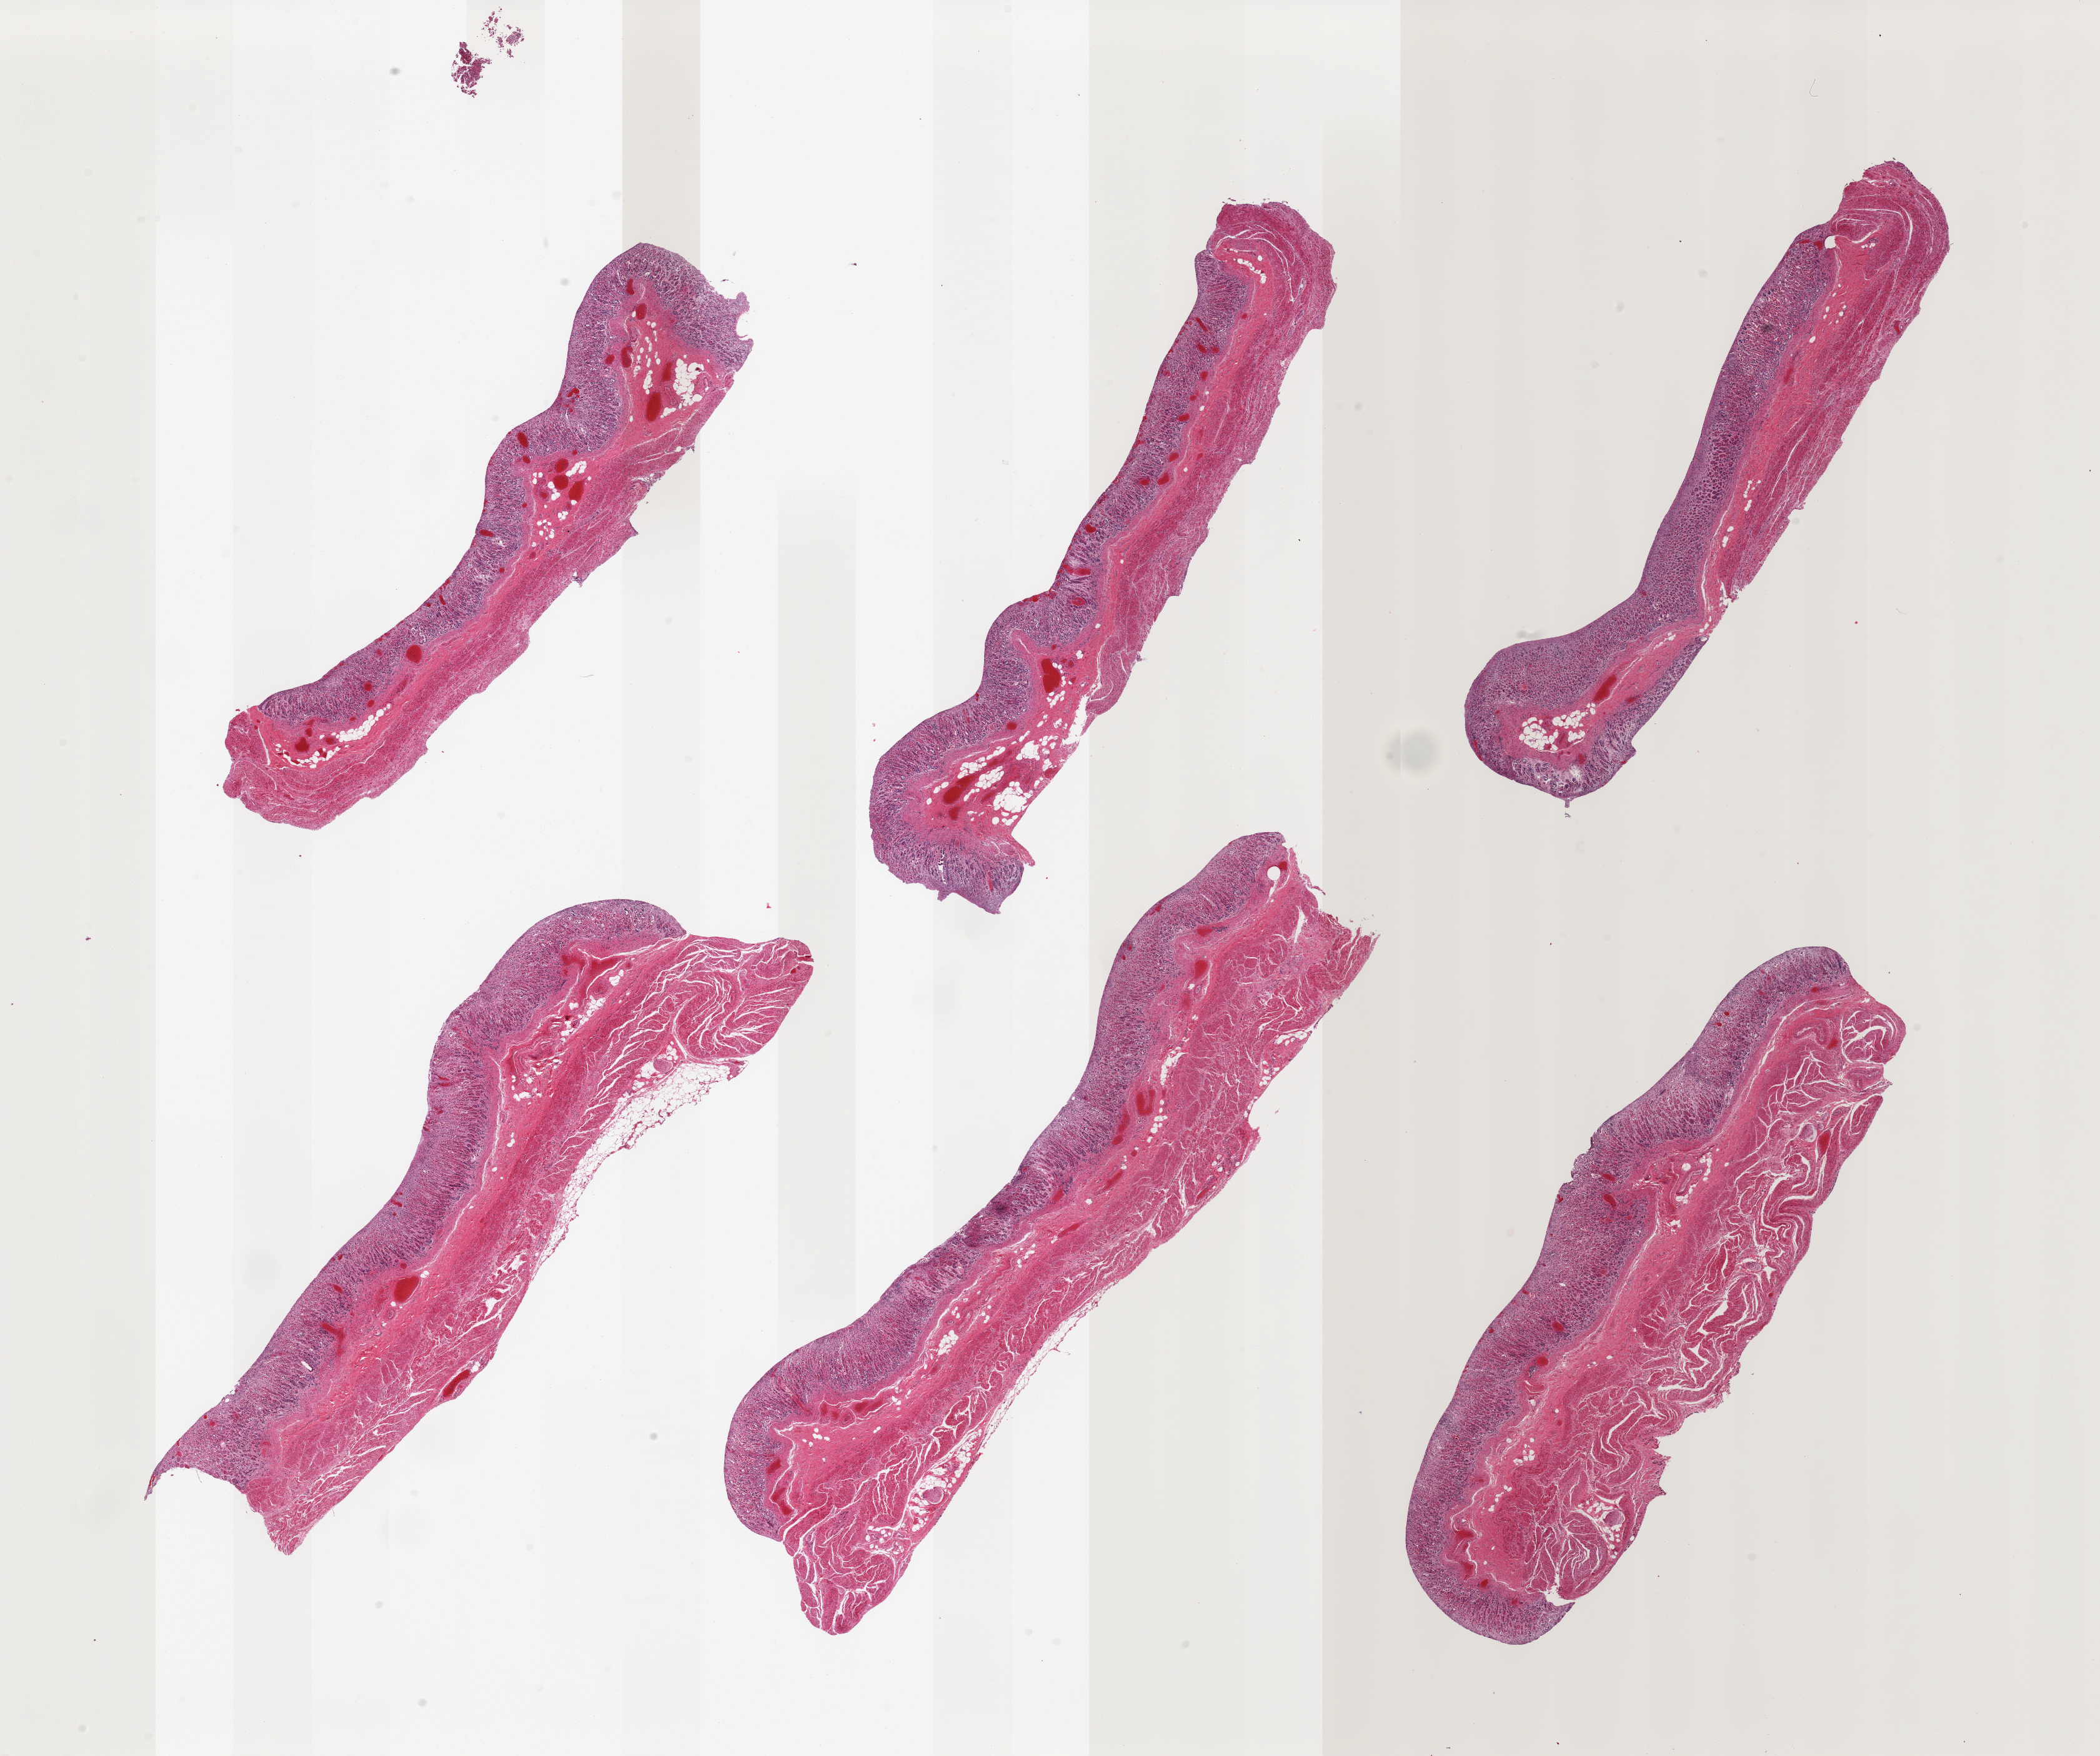
H&E whole-slide image — shown as a low-resolution overview of the whole scanned area (about 26.6 x 22.2 mm); PAXgene-fixed, paraffin-embedded tissue; section of stomach (target tissue); tissue donor sample. Donor: female.
Reviewer comment on this tissue sample: 6 pieces, target mucosa up to ~0.7mm, advanced autolysis.